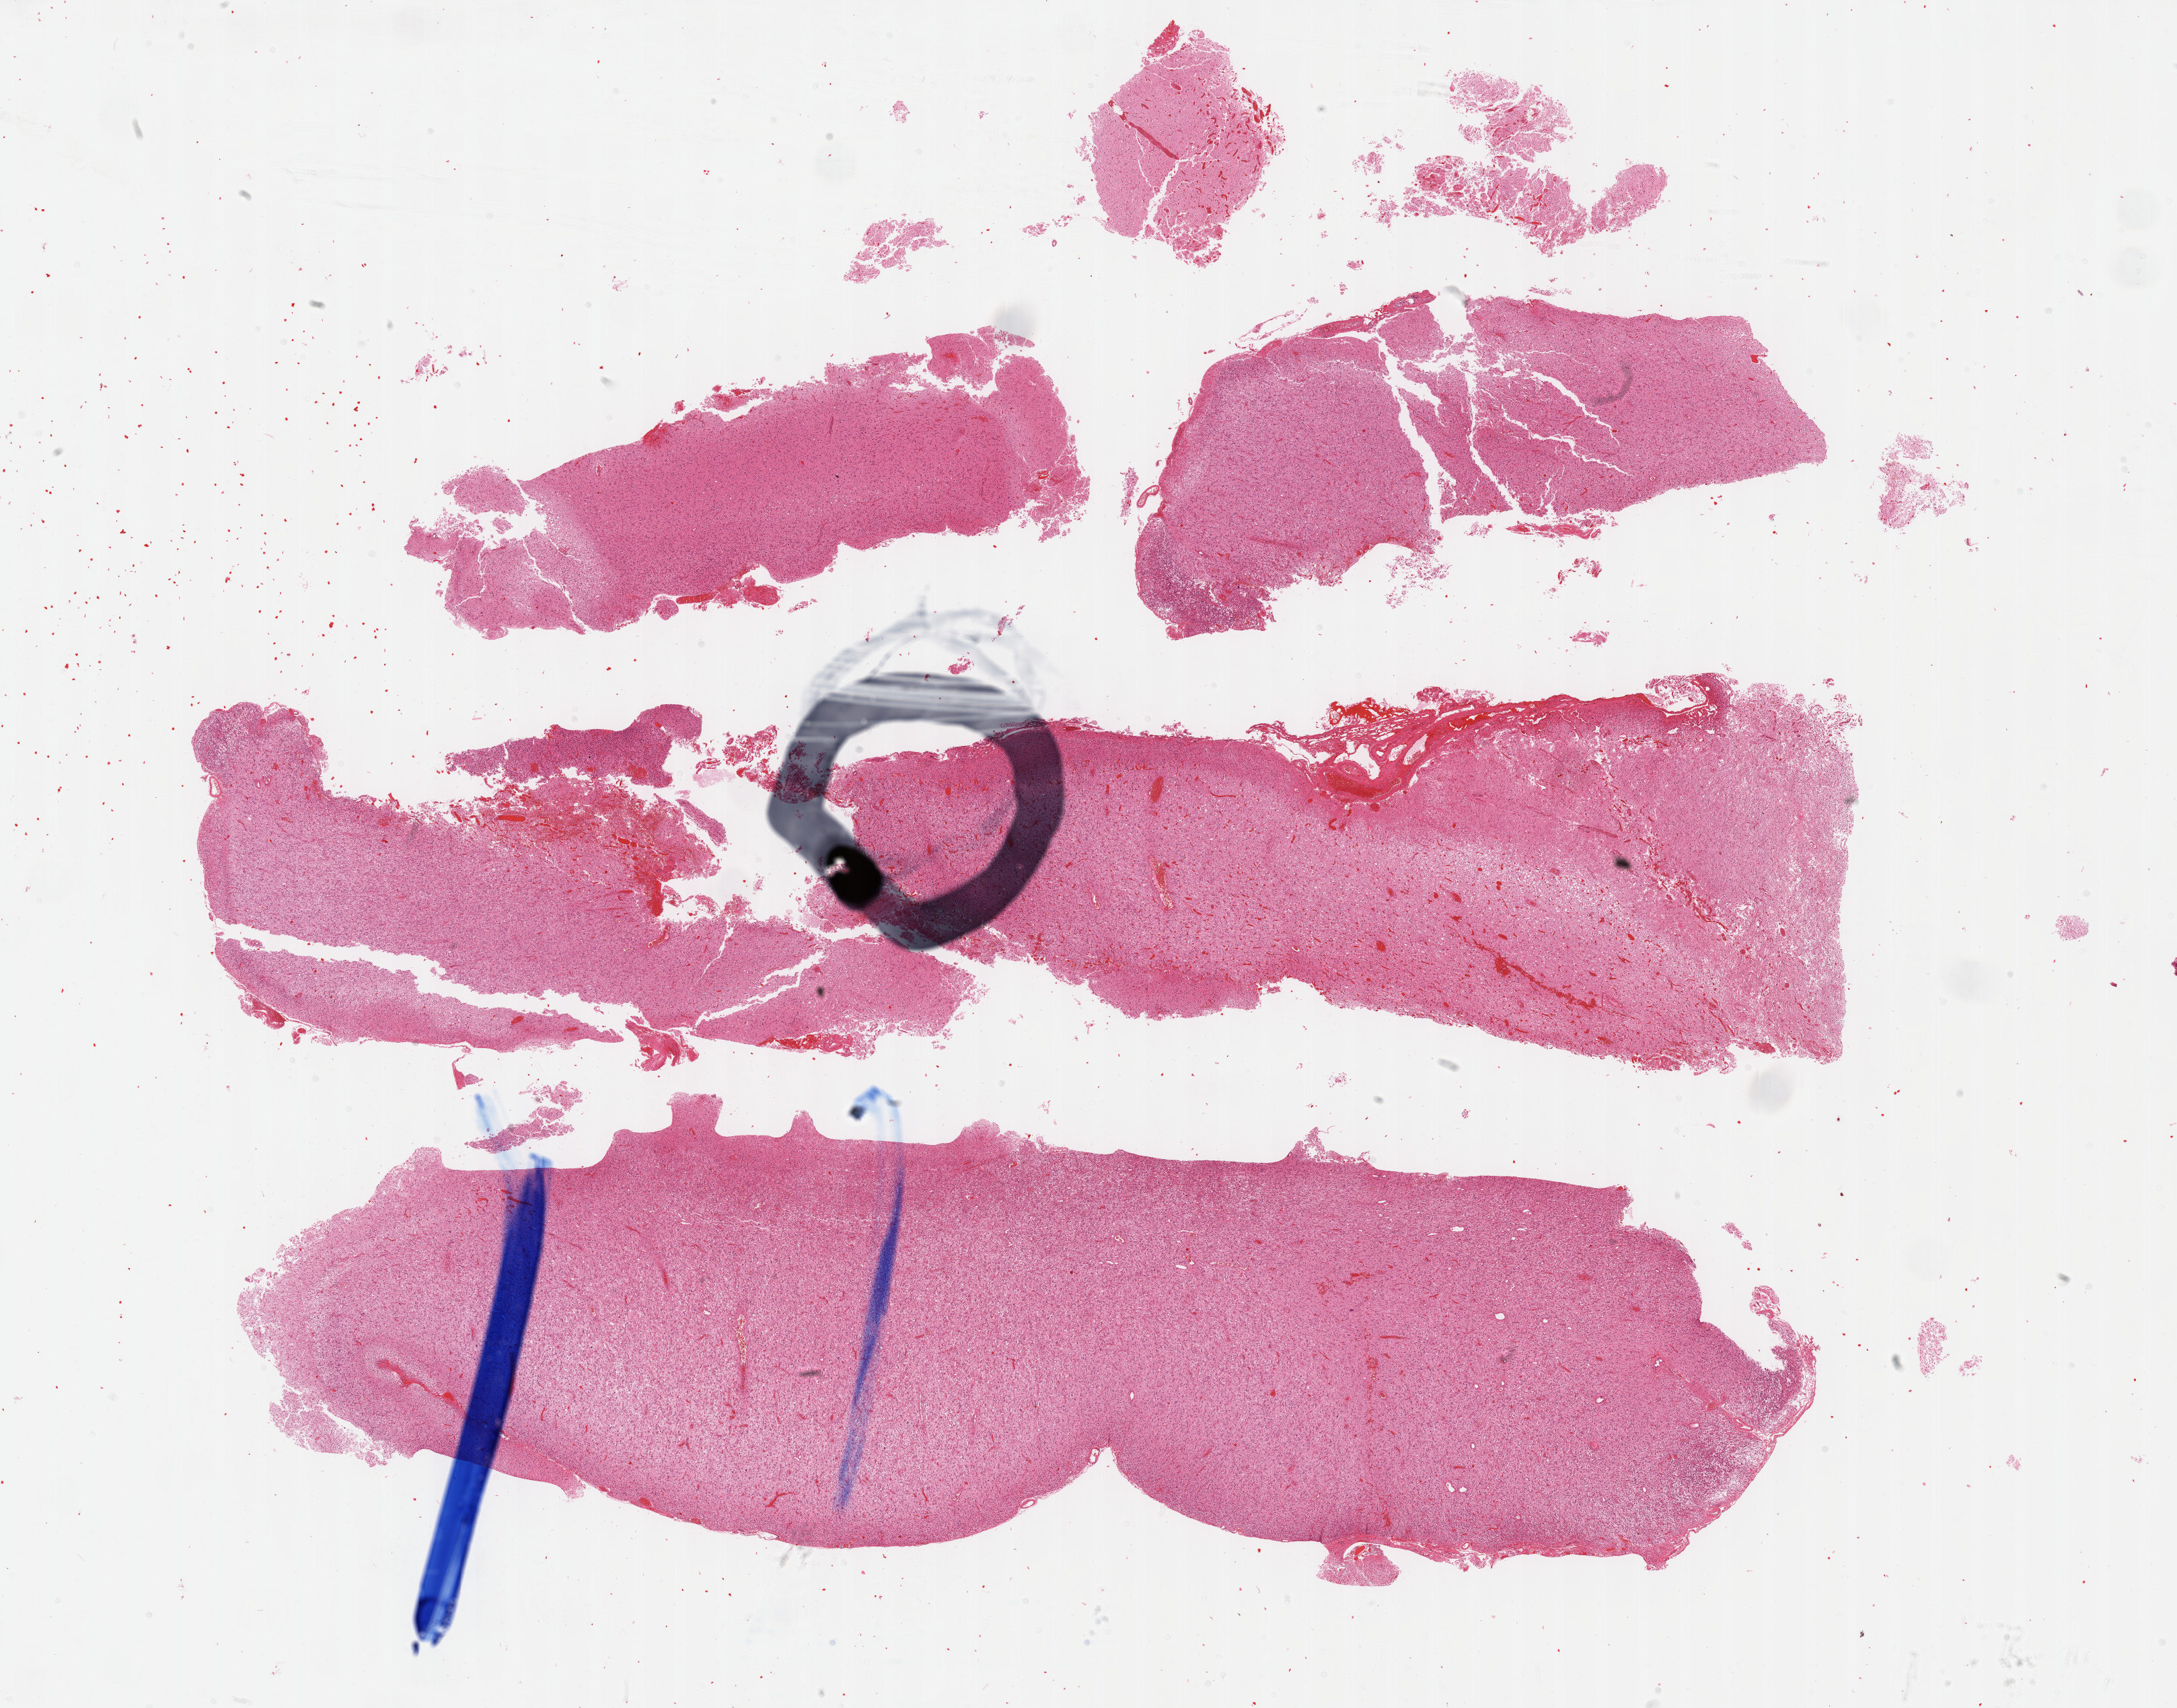
H&E-stained whole-slide image, low-resolution overview of the scanned area, about 26.2 x 20.5 mm. Formalin-fixed paraffin-embedded (FFPE) diagnostic section. Primary tumour sample from the brain. Patient: female, age at initial diagnosis 48 years. Histologic grade: G3 (poorly differentiated).
• laterality: left
• pathologic diagnosis: Astrocytoma, anaplastic (cerebrum)